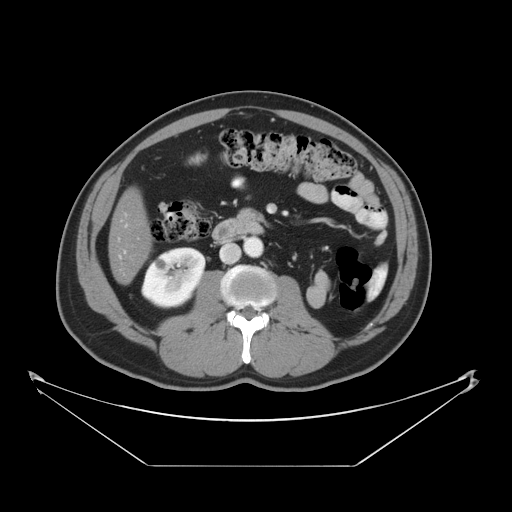
Contrast-enhanced abdominal CT, one axial slice; position 13 of 46 along the scan axis; intravenous contrast given; soft-tissue window (W 400 / L 40 HU); 5 mm slice thickness; 512 × 512 image matrix. Male patient, age 57 years. Case-level facts recorded for this patient, not image findings: diagnosis: colorectal cancer liver metastases, imaged before liver resection; multiple liver metastases: no; largest metastasis: 3.3 cm.
Structures marked on this image (expert manual segmentation):
- liver: bounding box (x1, y1, x2, y2) in pixels: (110, 192, 149, 283)
- planned liver remnant (the part of the liver to remain after resection): (110, 192, 149, 283)